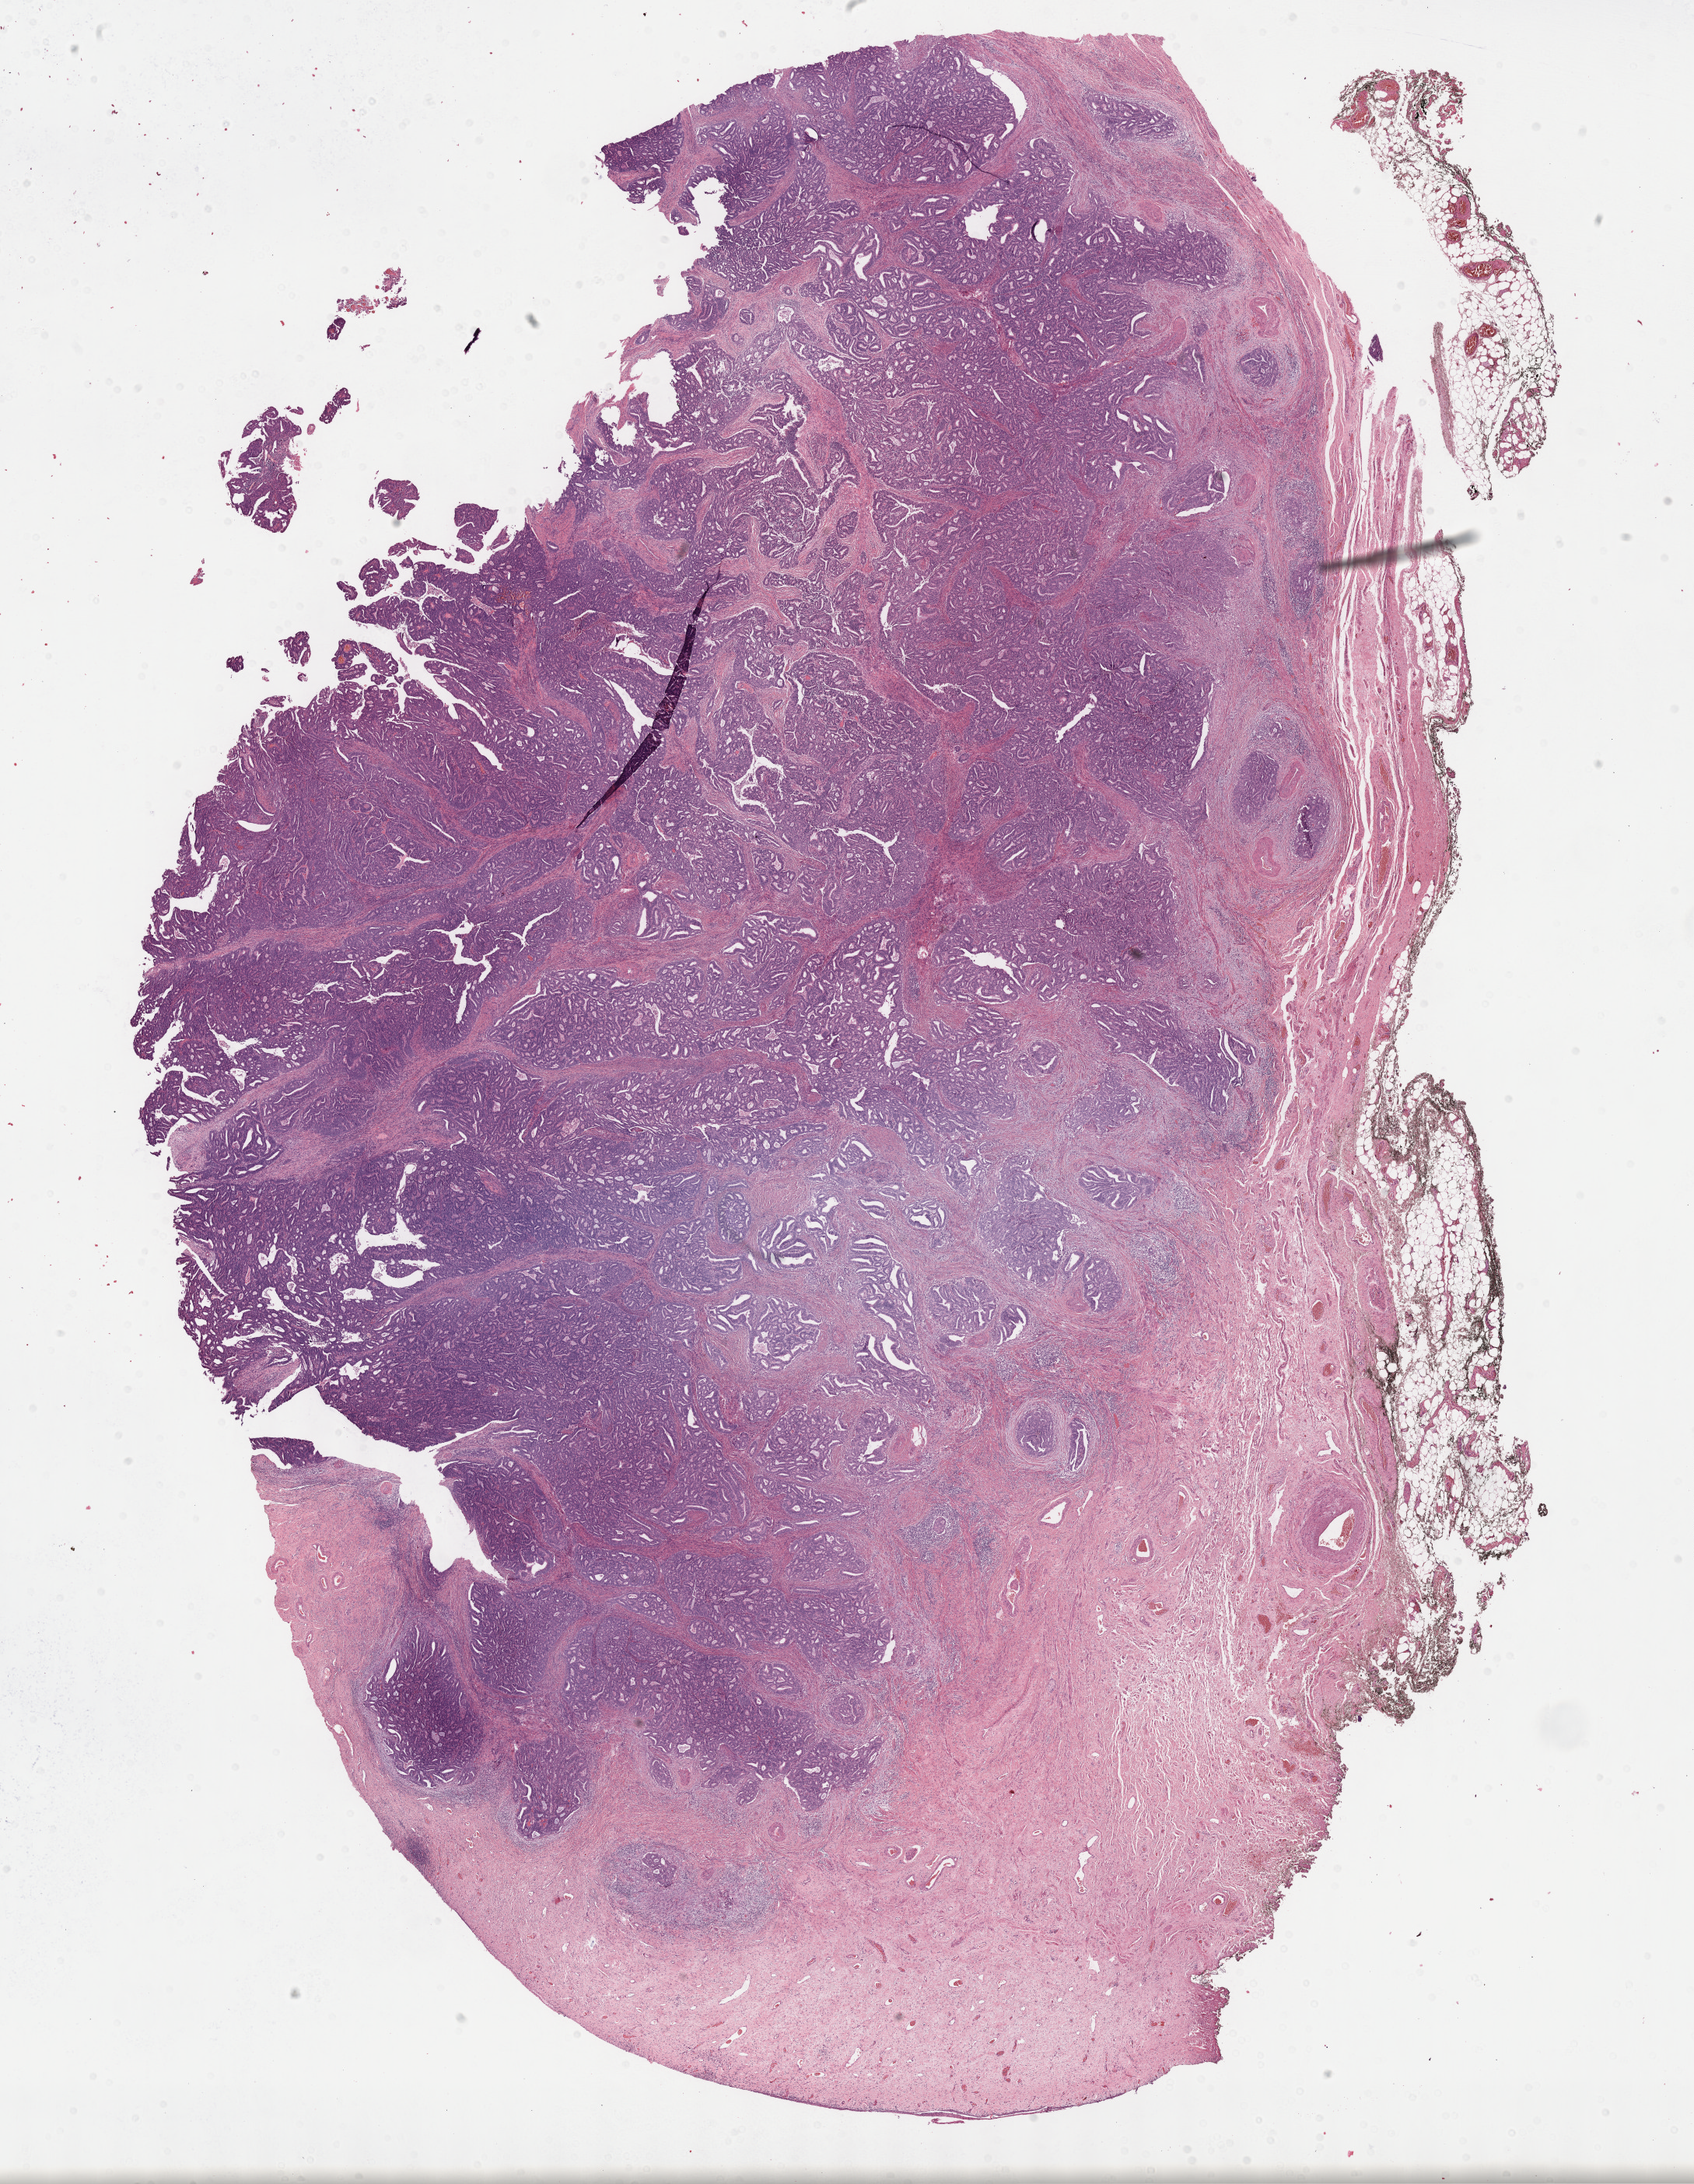
Digitized H&E-stained tissue section (whole slide) — low-resolution overview of the scanned area, about 17.6 x 22.7 mm (from a 40x scan); FFPE section; cervix, primary tumour sample. Female, age 61 years at initial diagnosis. Histologic grade: G2 (moderately differentiated).
- FIGO stage: IB1
- lymph nodes positive (case pathology): 0 of 26 examined
- diagnosis: Mucinous adenocarcinoma, endocervical type (cervix uteri)